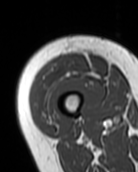
MRI of an extremity soft-tissue mass, one axial slice; position 20 of 99 along the scan axis; MR volume resampled by the dataset authors to the PET/CT grid (not the native acquisition matrix); 3.27 mm slice thickness; 138 × 172 image matrix, field of view 135 × 168 mm. Female patient. From the clinical record (not read from this slice): histological type: pleiomorphic undifferentiated sarcoma; grade: high; site of the primary tumour: right quadricep.
Structures marked on this image (expert contour drawn on MRI and transferred to this co-registered scan by the dataset authors):
- gross tumour volume including surrounding oedema: box from (x=32, y=54) to (x=86, y=119) px